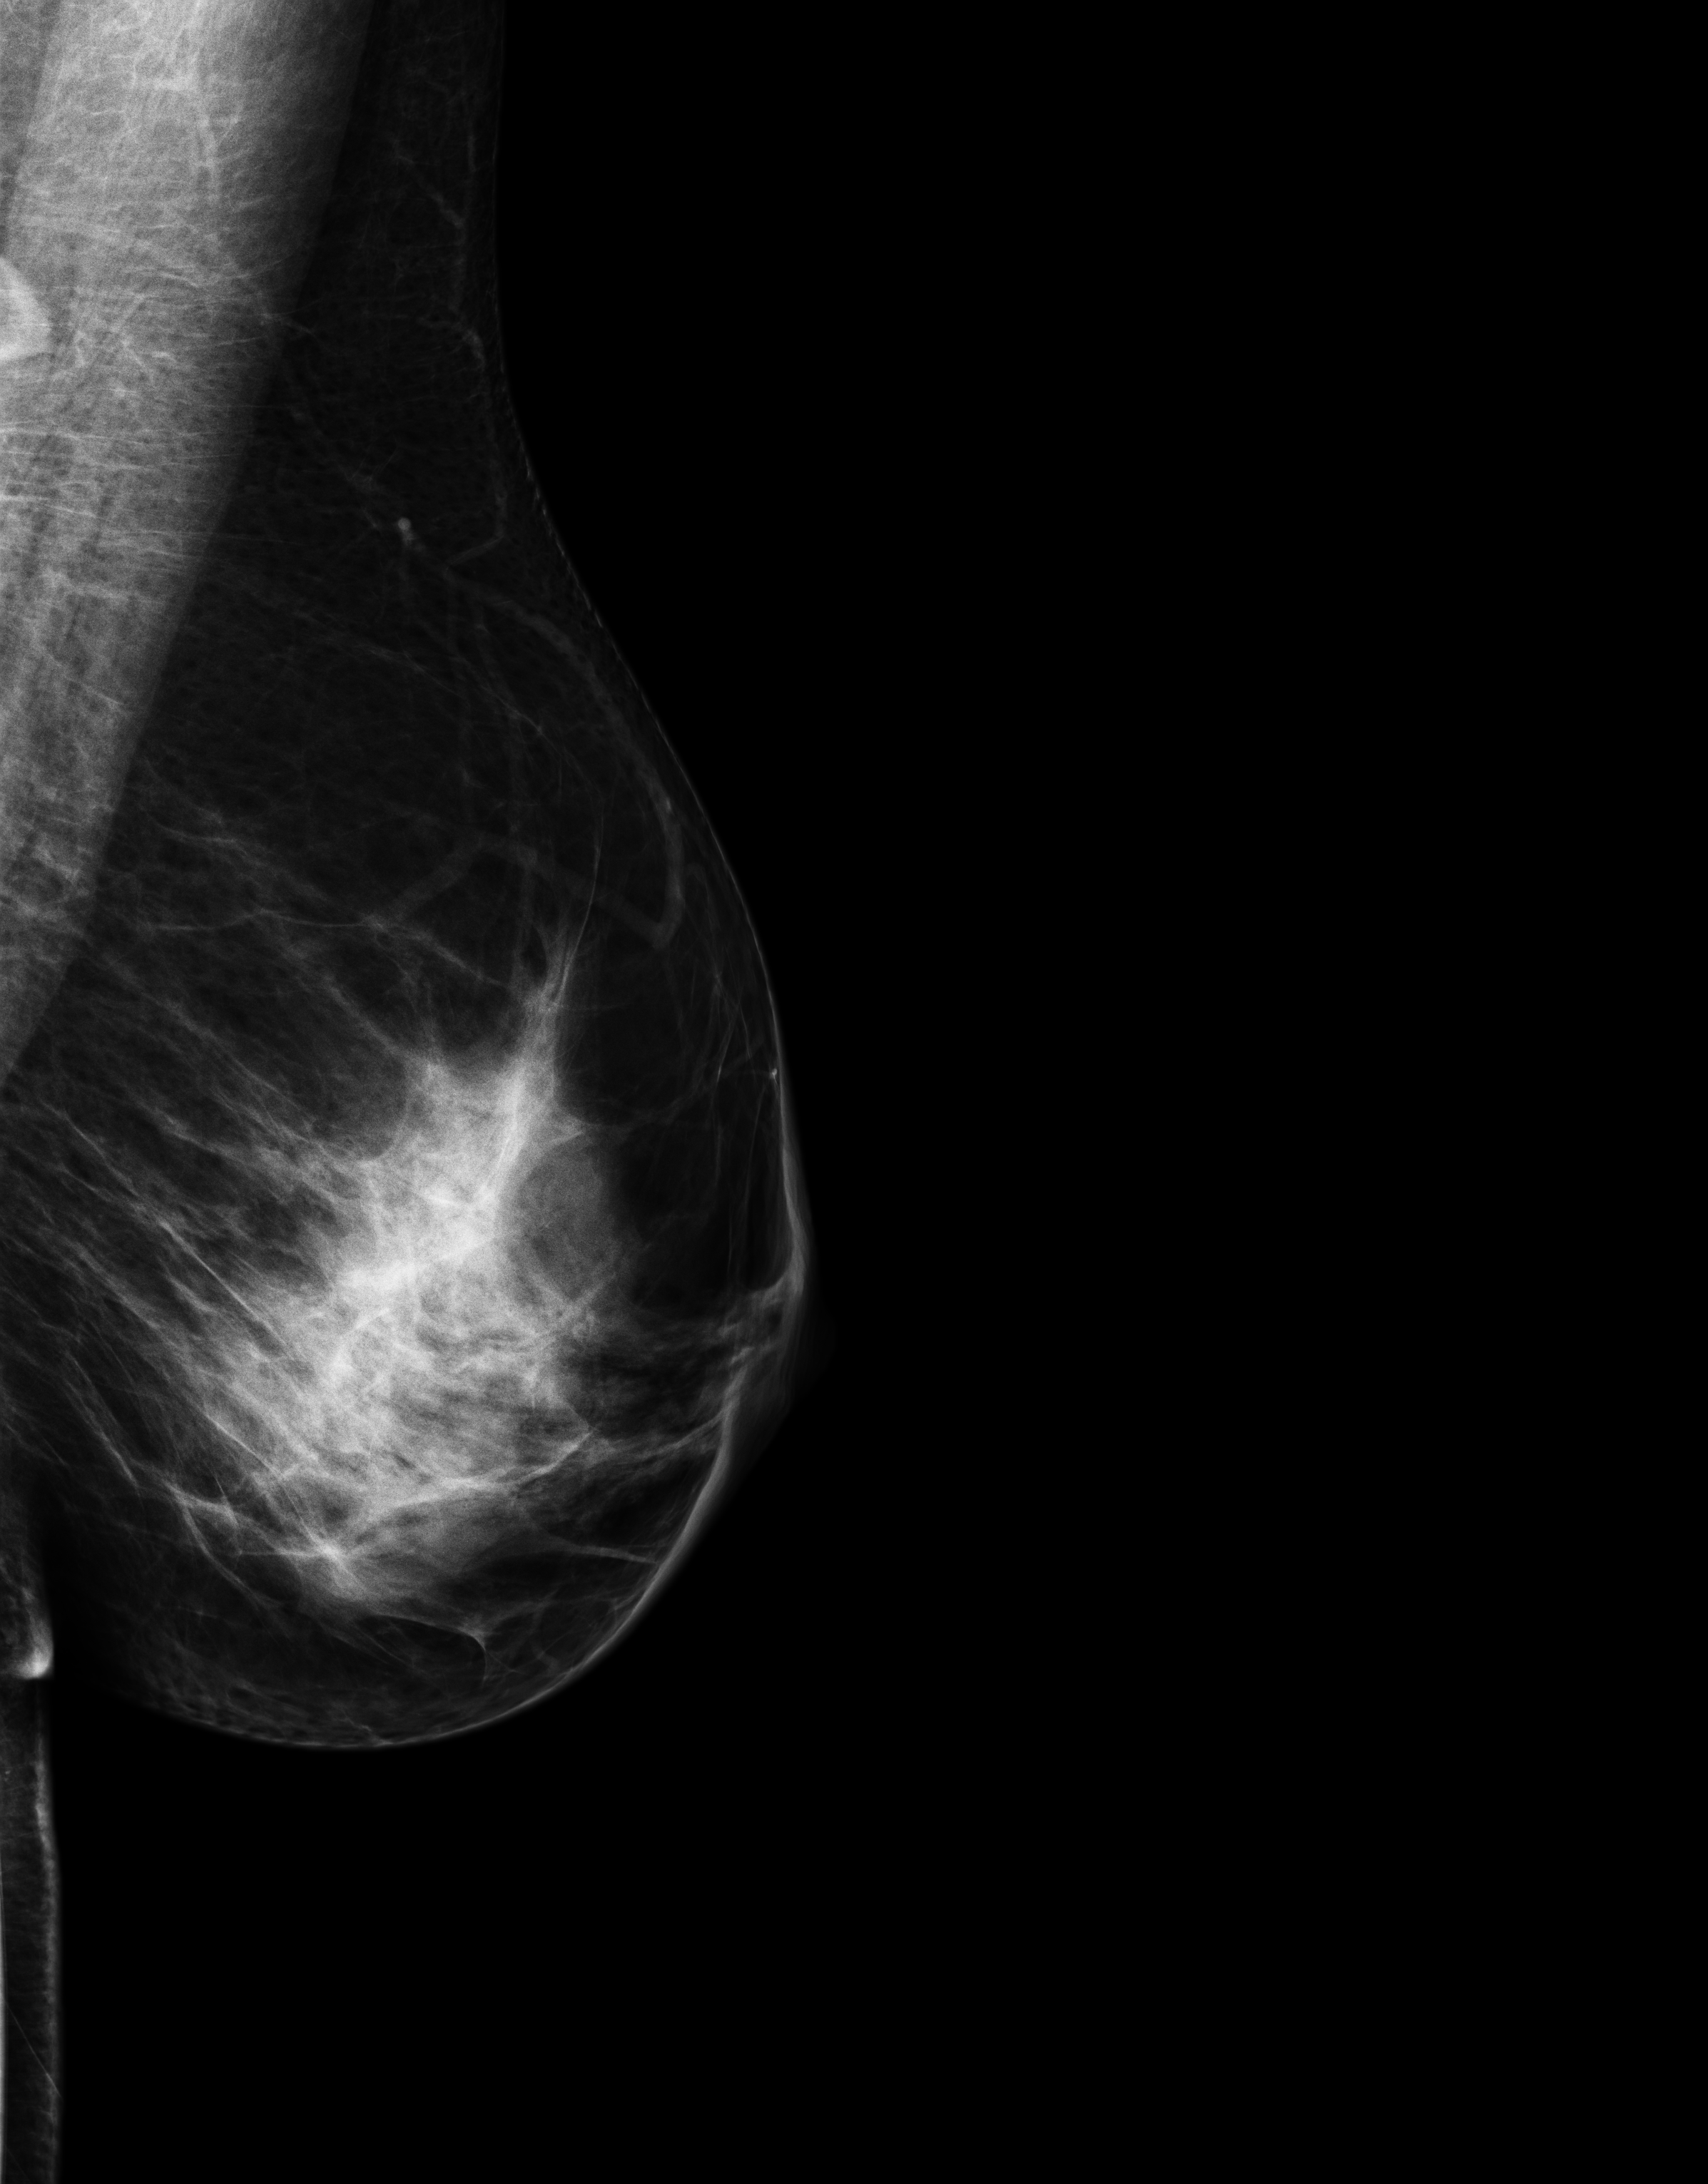
Digital mammogram (FFDM), left breast, mediolateral oblique (MLO) view, annual screening mammography examination, compressed breast thickness 84 mm. Patient aged 44 years (female).
BI-RADS breast density category at the screening exam (both breasts, scale 1–4): 3. Final BI-RADS assessment for this screening round (tomosynthesis exam, both breasts): category 1. Recall: no recall after this screen.